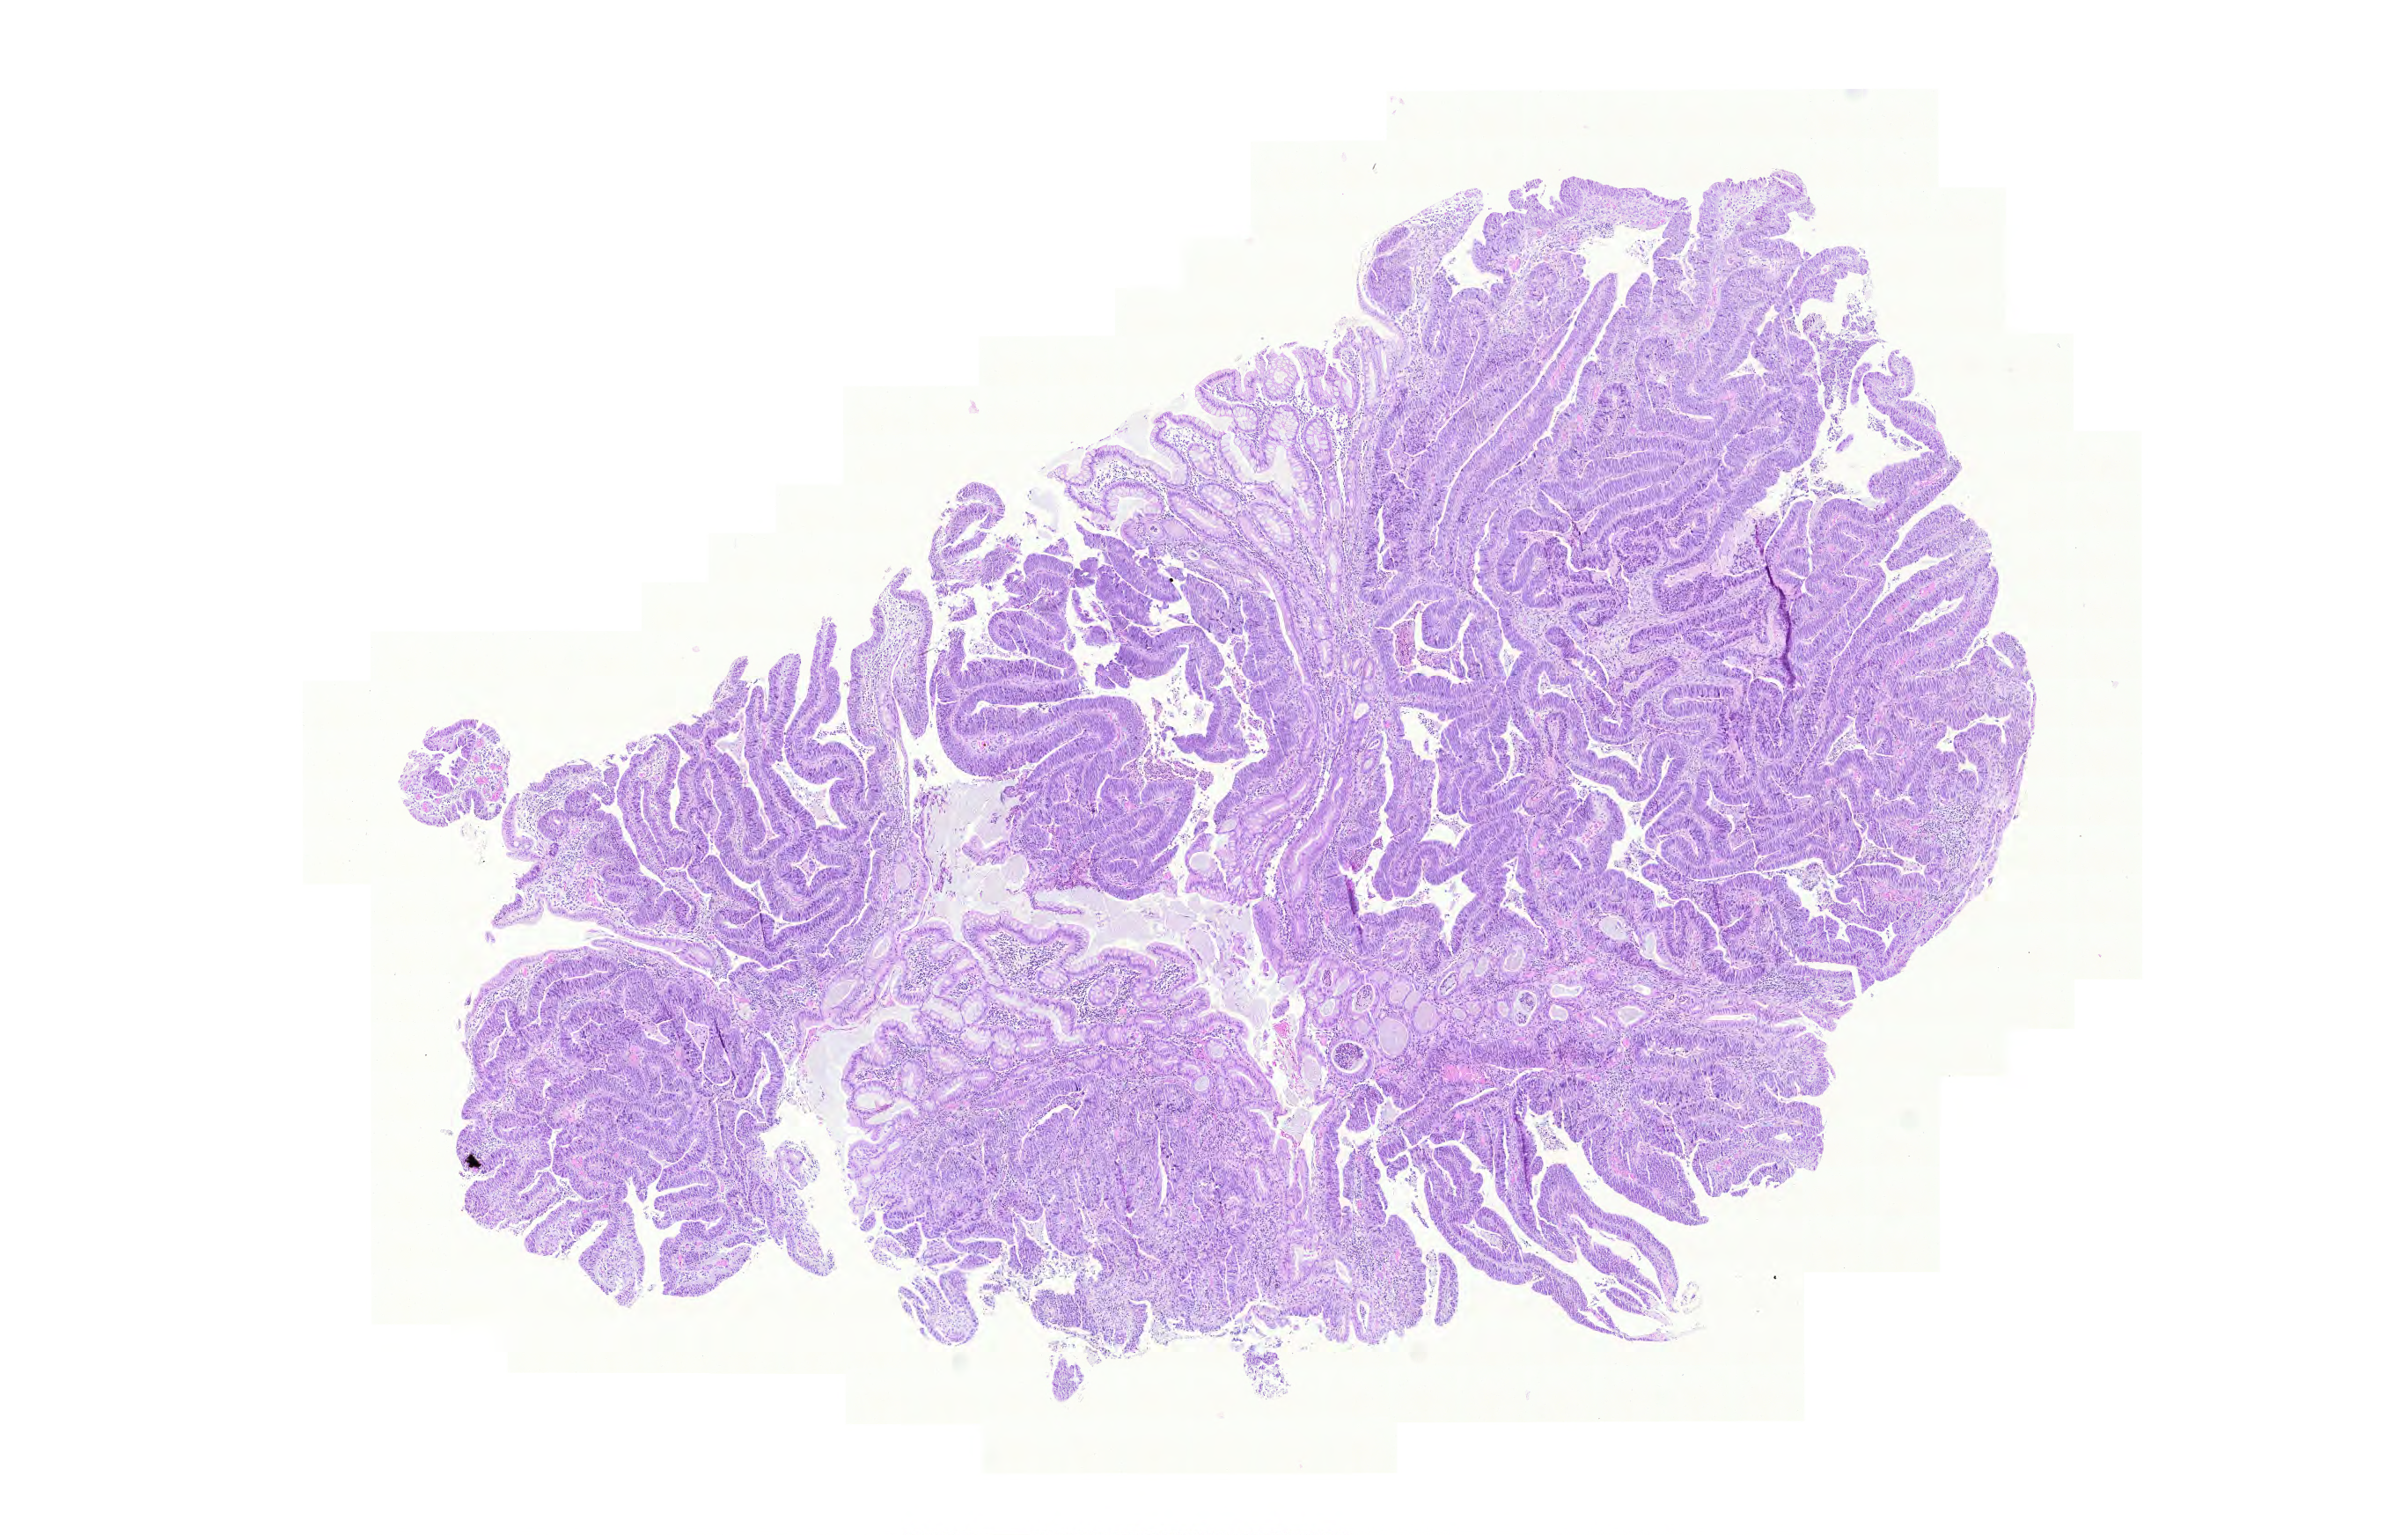
H&E whole-slide image — shown as a low-resolution overview of the whole scanned area (about 10.2 x 6.5 mm, acquisition: 20x scan), formalin-fixed paraffin-embedded (FFPE) diagnostic section, sample: primary tumour, colon. Female, age 60 years at initial diagnosis.
- AJCC pathologic stage: III (5th edition)
- TNM: T2 N1 M0
- histologic diagnosis: Adenocarcinoma, NOS (sigmoid colon)
- lymph nodes positive (case pathology): 1 of 26 examined